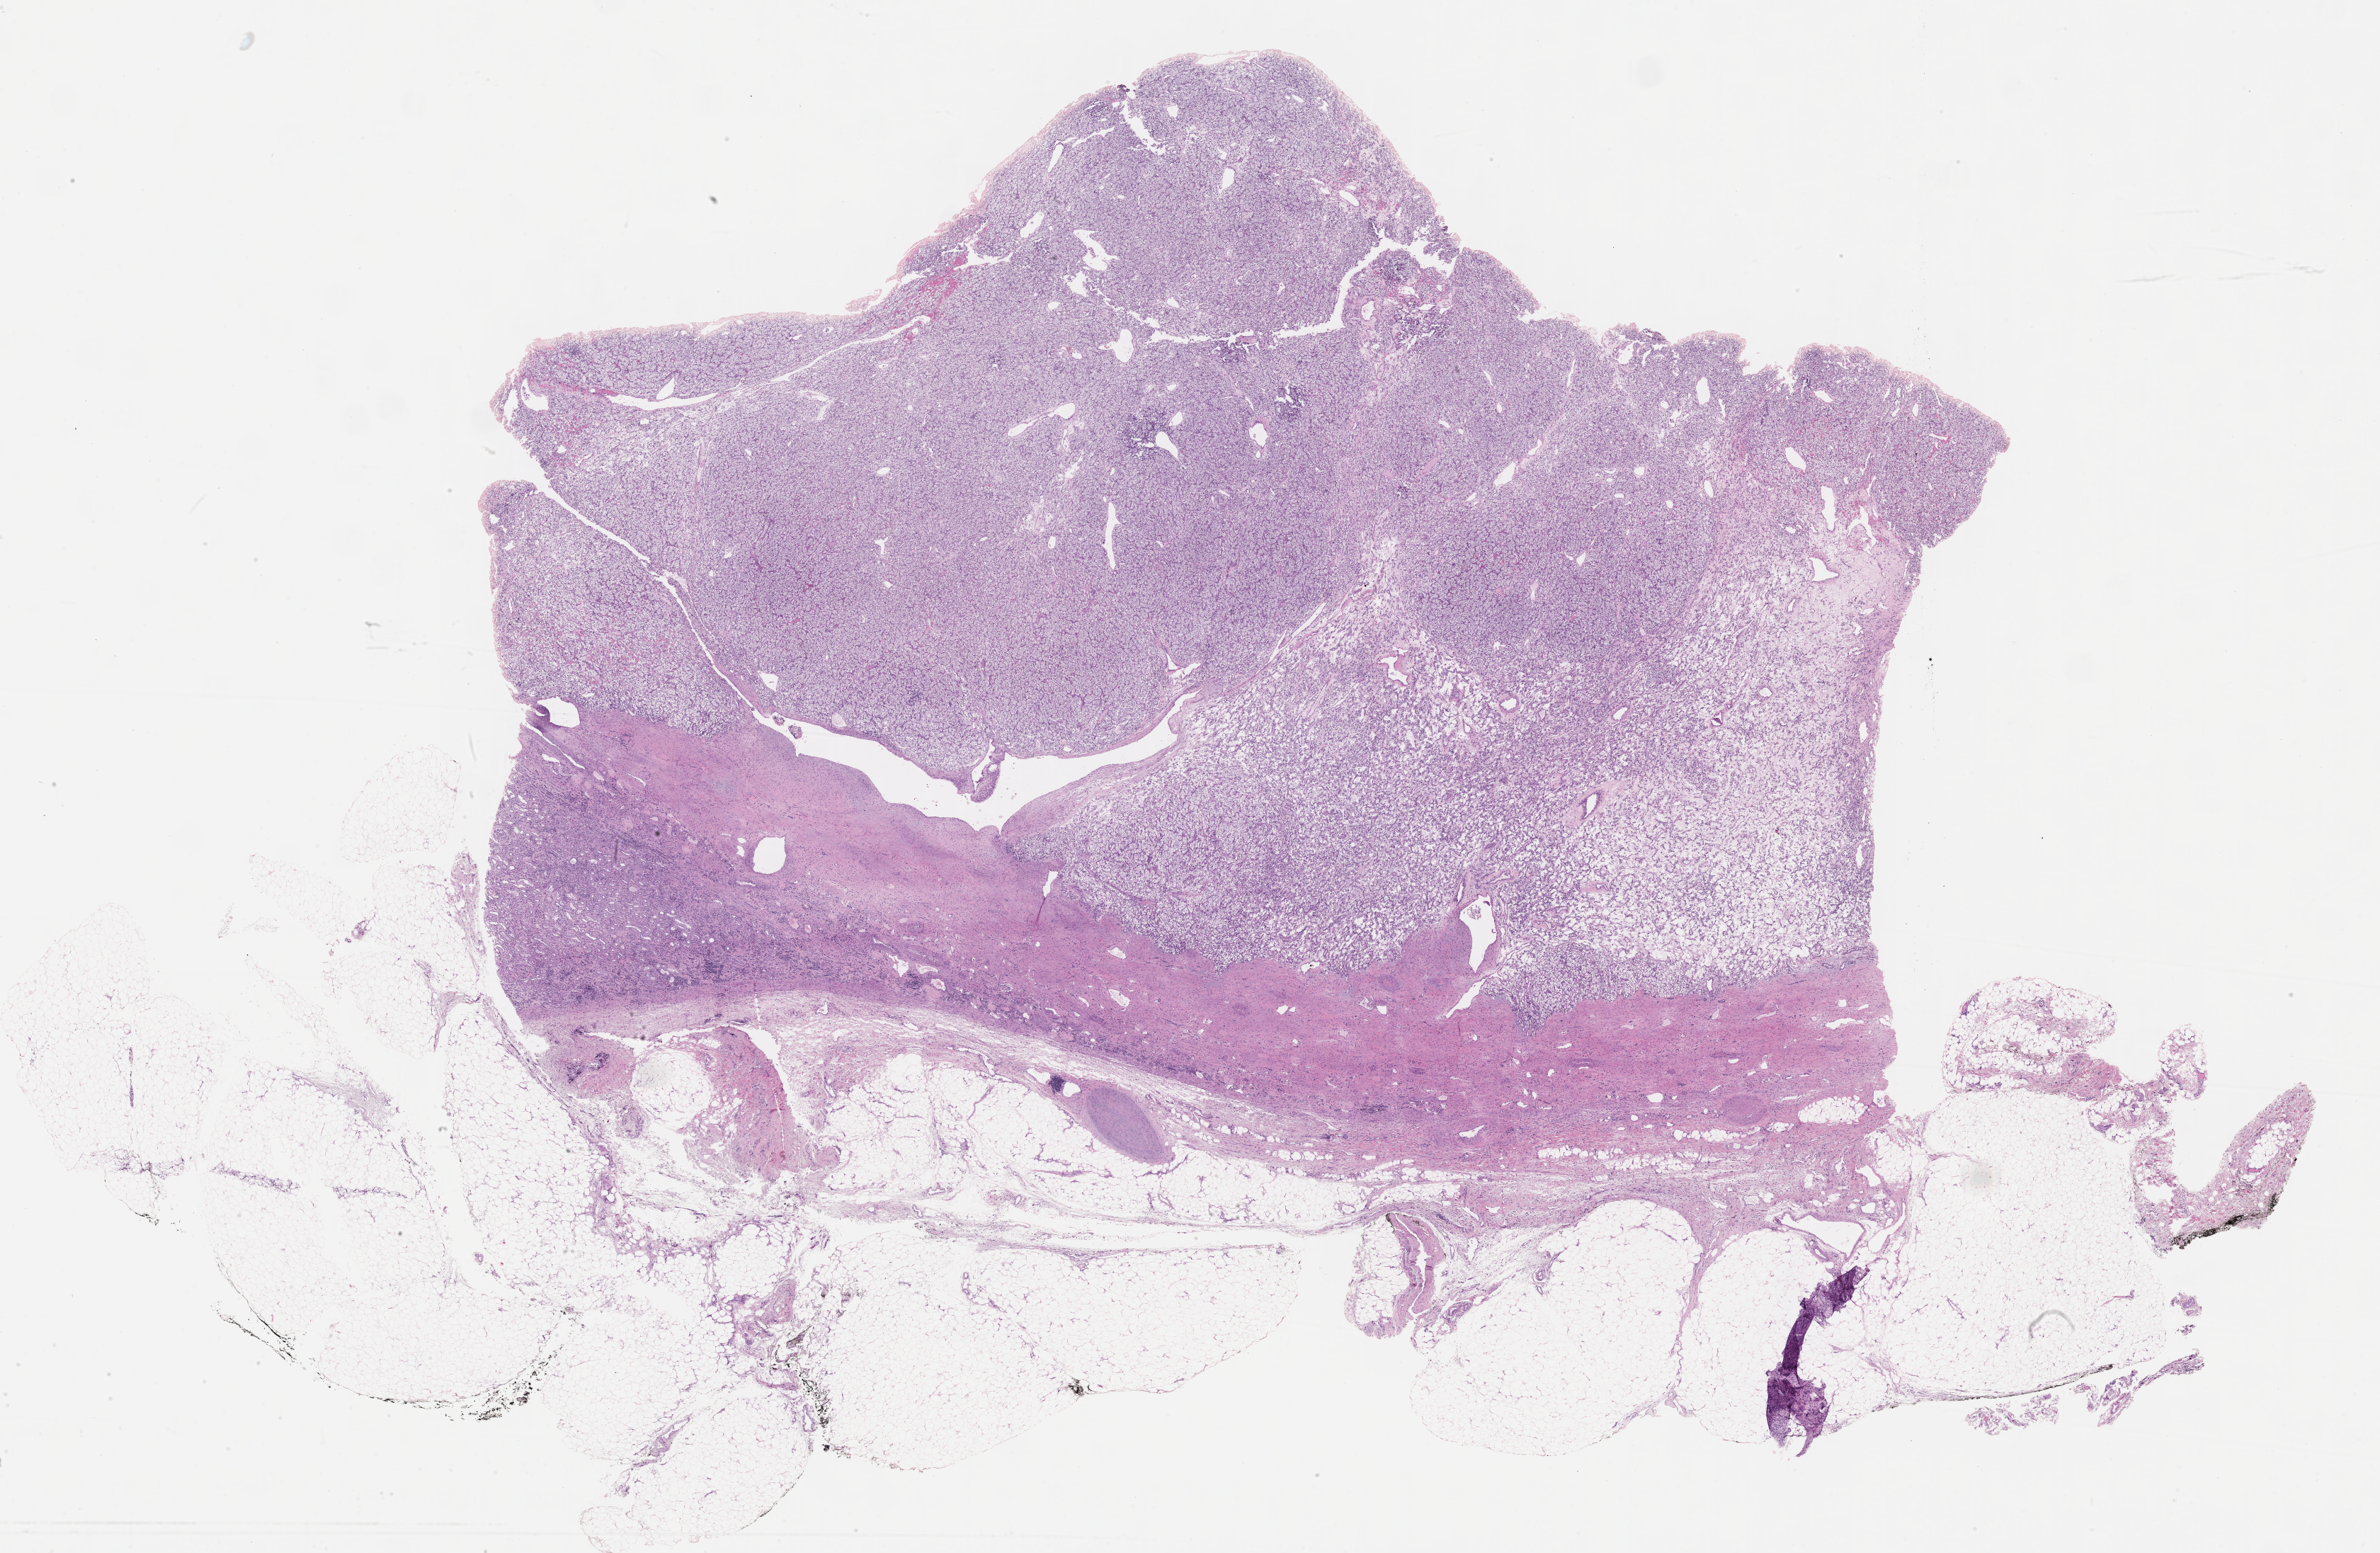
Whole-slide histology image, Hematoxylin and eosin (H&E) stained, a low-resolution overview of the entire scanned area, about 27.2 x 17.7 mm (acquisition: 40x scan). Formalin-fixed paraffin-embedded (FFPE) diagnostic section. Kidney, primary tumour sample. Patient: female, age at initial diagnosis 49 years. Histologic grade: G2 (moderately differentiated).
Diagnosis: Clear cell adenocarcinoma, NOS. Laterality: left. AJCC pathologic stage: II (7th edition).